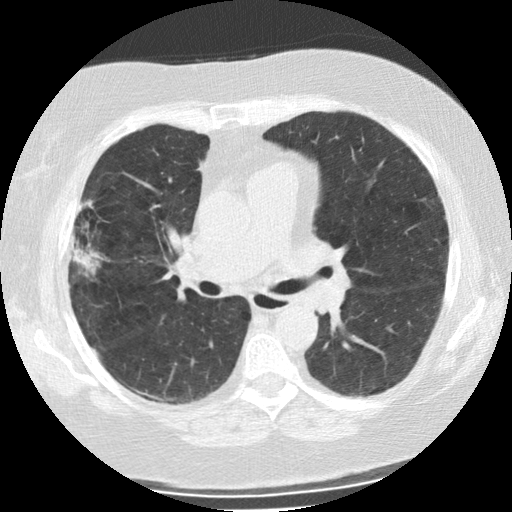
Axial slice from a low-dose chest CT screening exam; second screening round (one year after baseline); lung window (W 1500 / L -600 HU); slice 92 of 225 in the series; 512 × 512 image matrix, field of view 320 × 320 mm. Female, age 73 years at enrolment. Former smoker at enrolment.
Lesion marked by an expert reader, bounding box (x1, y1, x2, y2) in pixels: (56, 203, 106, 278). The screening reader recorded 2 non-calcified nodules or masses ≥4 mm on this exam (right upper lobe, left upper lobe); which of them this box marks is not recorded. Official screen result: positive, change unspecified: nodule(s) >= 4 mm or enlarging nodule(s), mass(es), or other non-specific abnormalities suspicious for lung cancer. Participant outcome: lung cancer diagnosed 47 days after this screen — bronchiolo-alveolar adenocarcinoma, NOS, right upper lobe, moderately differentiated (G2), stage IIIB (AJCC 6th edition), 21 mm at pathology.